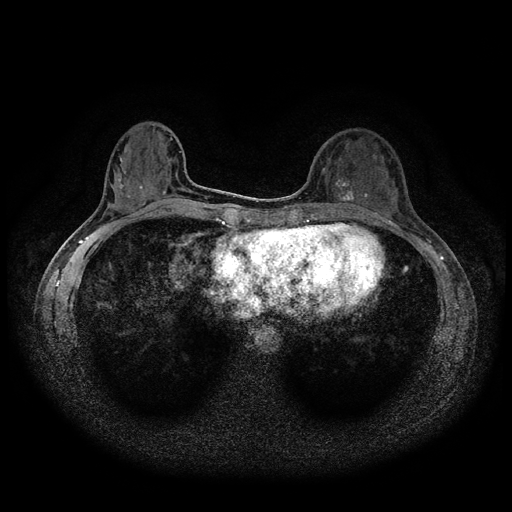
Breast MRI (dynamic contrast-enhanced, multi-phase), one axial slice. Position 36 of 116 along the scan axis. Dynamic contrast-enhanced series, time point 2 of 5 at this slice position (early post-contrast). 1.5 T. TE 2.7 ms, TR 5.4 ms. 512 × 512 image matrix. Female patient, age 36 years.
Outlined on this slice (semi-automatic segmentation, software-assisted and operator-edited):
- breast lesion (labelled benign in the annotation): box from (x=335, y=177) to (x=356, y=202) px